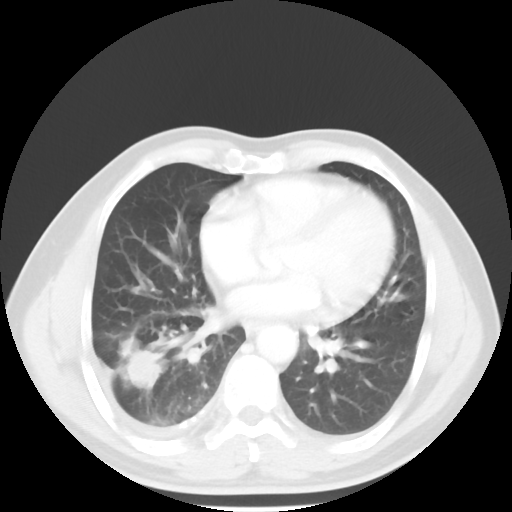
Chest CT, one axial slice. Slice 23 of 56 in the series (ordered by position). 120 kVp. Lung window (W 1500 / L -600 HU). 5 mm slice thickness. 512 × 512 image matrix, field of view 344 × 344 mm. Male patient, age 56 years. Case-level facts recorded for this patient, not image findings: clinical TNM (as recorded): T2 N3 M1.
Annotated regions visible in this slice (bounding box drawn by a radiologist):
- lung tumour (recorded histology: adenocarcinoma): bounding box (x1, y1, x2, y2) in pixels: (119, 343, 163, 392)